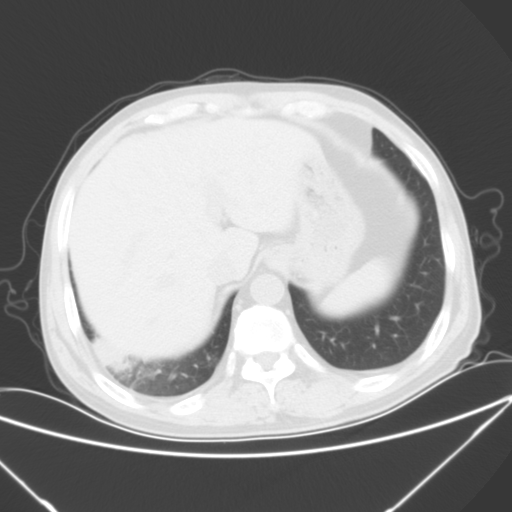
Chest CT, one axial slice; position 13 of 57 along the scan axis; lung window (W 1500 / L -600 HU); 512 × 512 image matrix. Male patient, age 54 years. Case-level facts recorded for this patient, not image findings: clinical TNM (as recorded): T2 N1 M0; histopathological grade: G3.
Outlined on this slice (rectangle marked by the reading radiologist):
- lung tumour (recorded histology: adenocarcinoma): box from (x=90, y=332) to (x=128, y=371) px